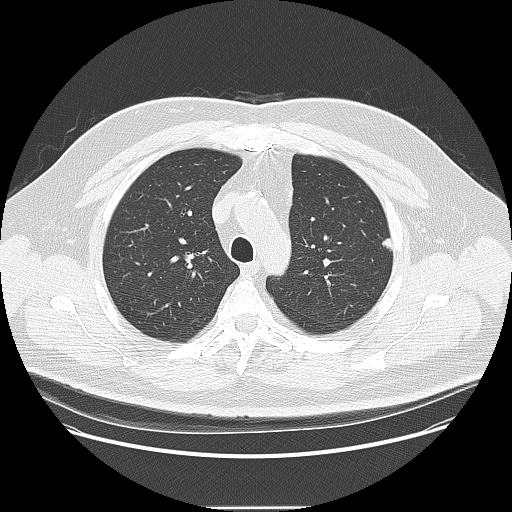
Low-dose screening chest CT, one axial slice. Slice 113 of 157 in the series (ordered by position). Lung window (W 1500 / L -600 HU). 2.5 mm slice thickness. 512 × 512 image matrix, field of view 410 × 410 mm.
Outlined on this slice (manually delineated by an expert):
- lesion 1 (tumor, upper lobe of left lung): bounding box <382,238,393,251> (left, top, right, bottom; pixels)